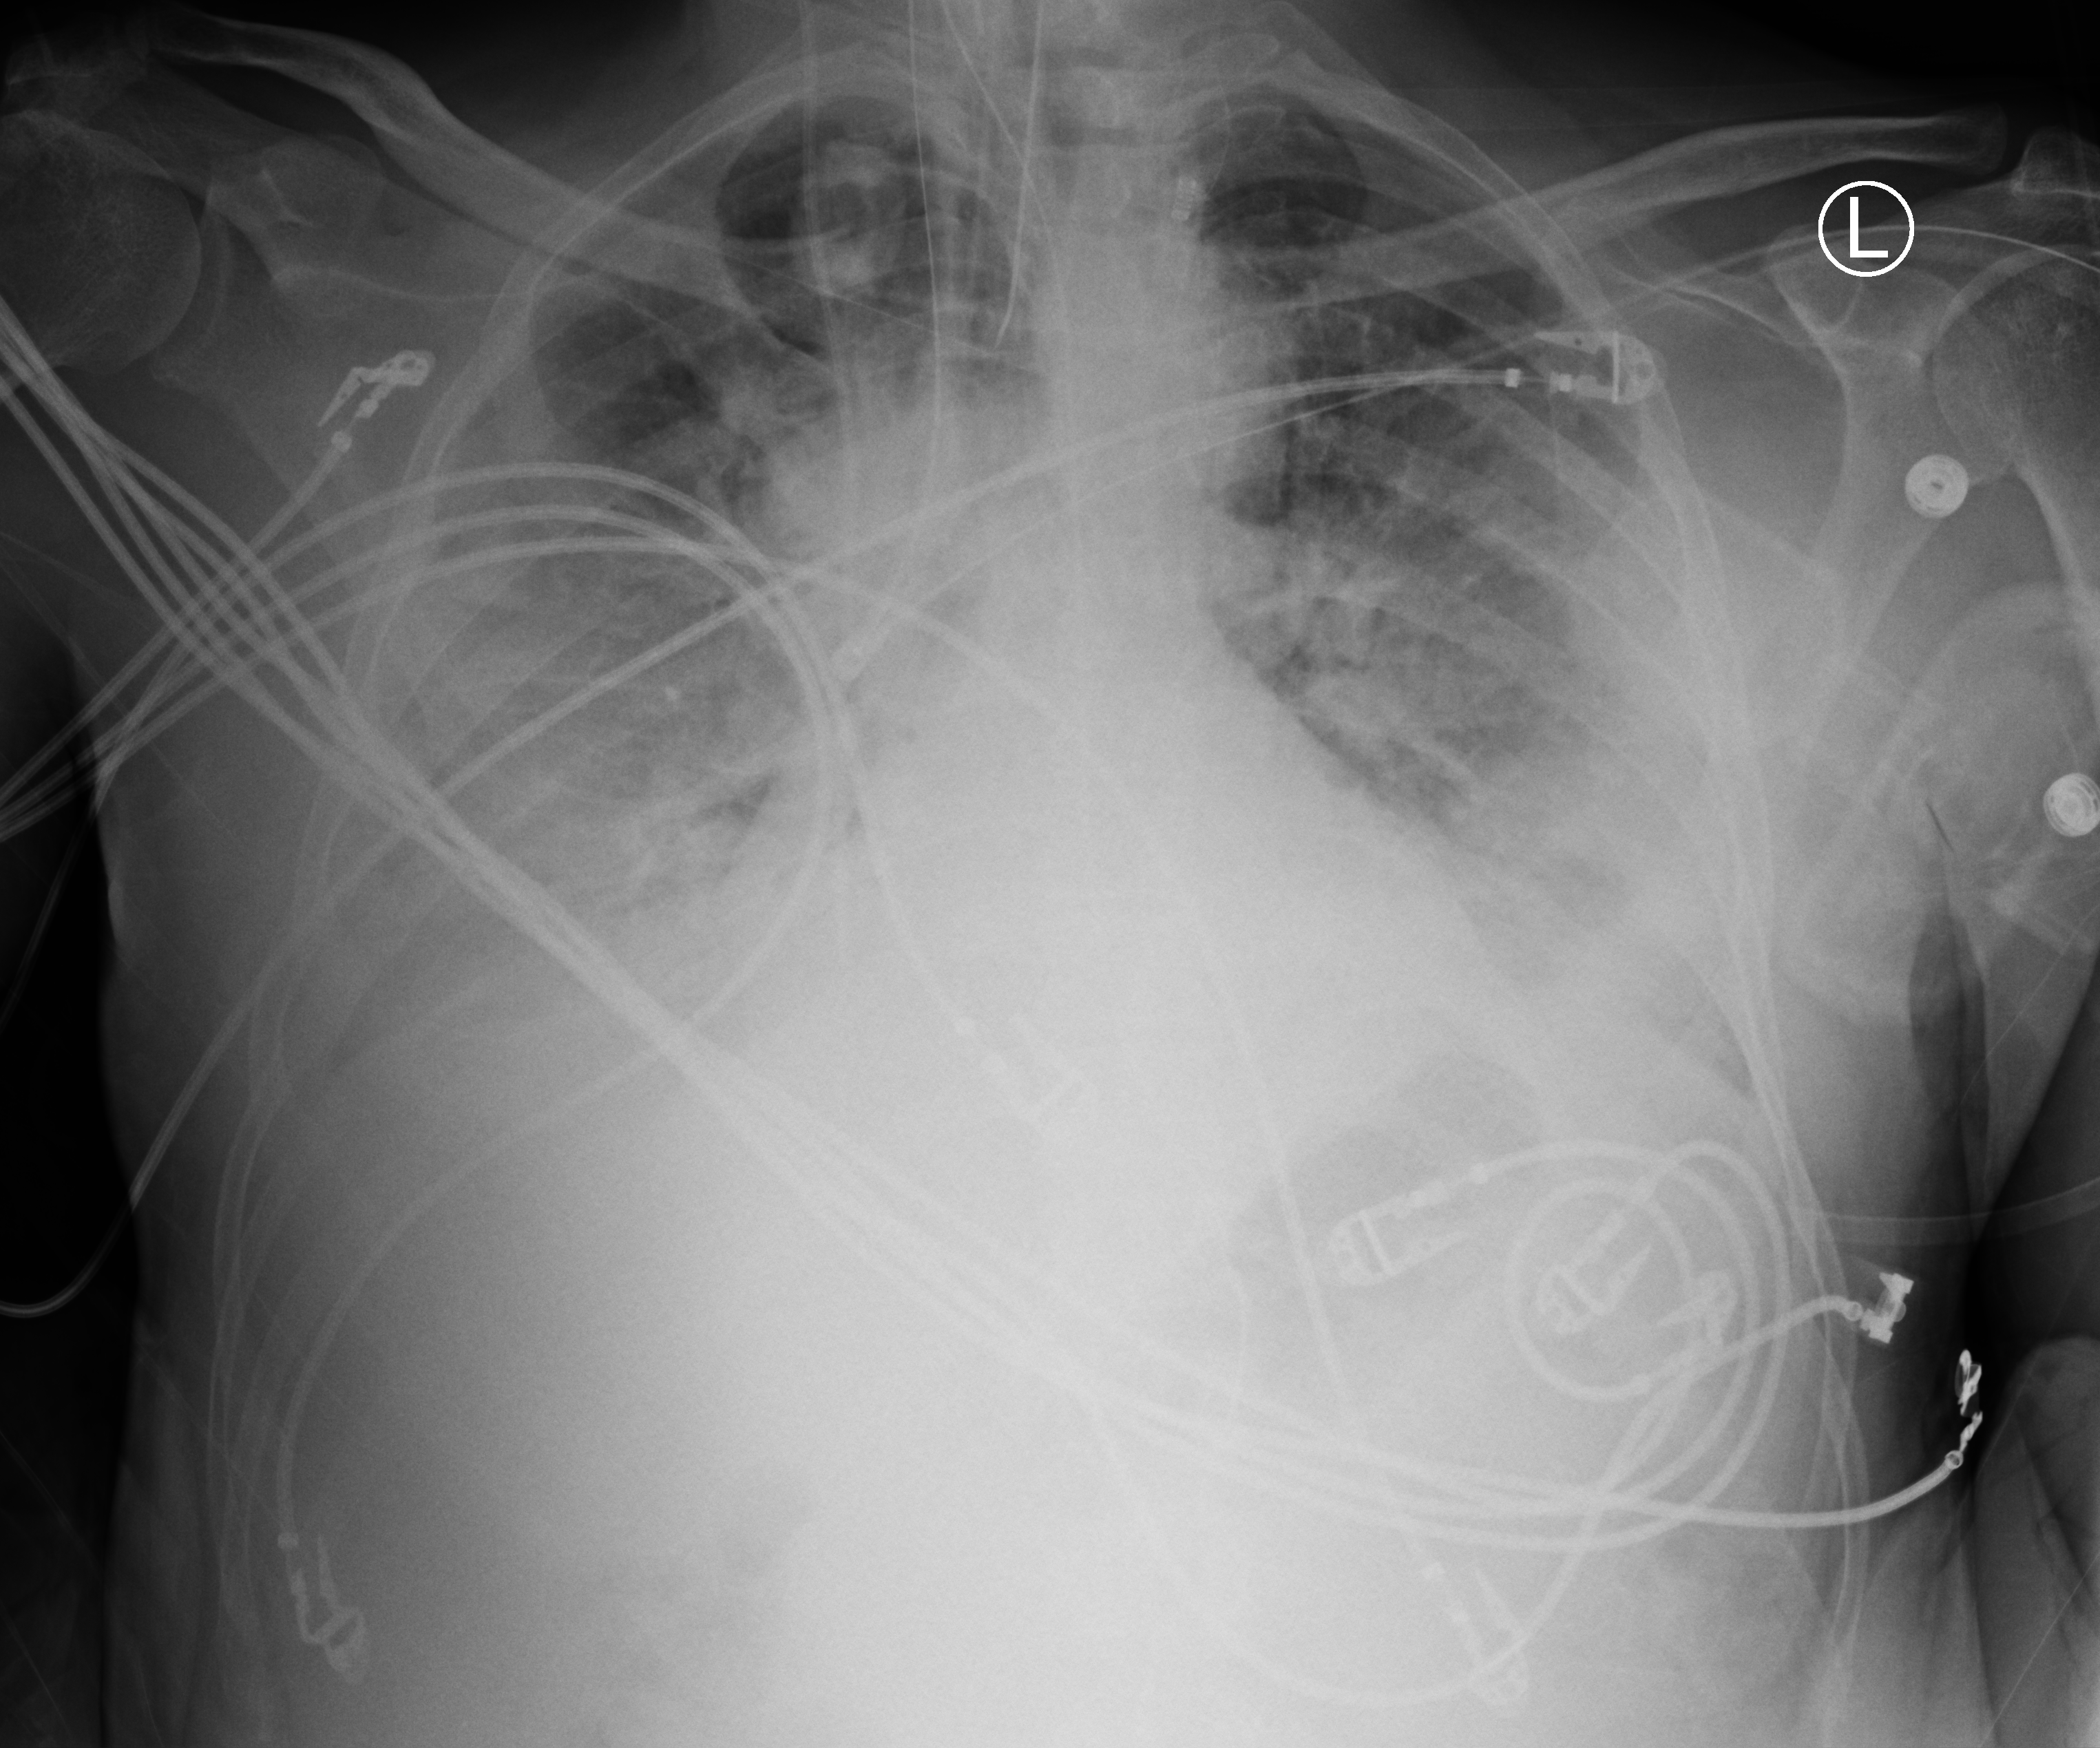
Portable chest radiograph; anteroposterior (AP) projection. Patient hospitalised with COVID-19; male, aged 18–59 years.
From the hospital-stay record, not from the radiograph (when in the stay this image was taken is not recorded): other chronic lung disease (admission record): no; diabetes (admission record): yes.